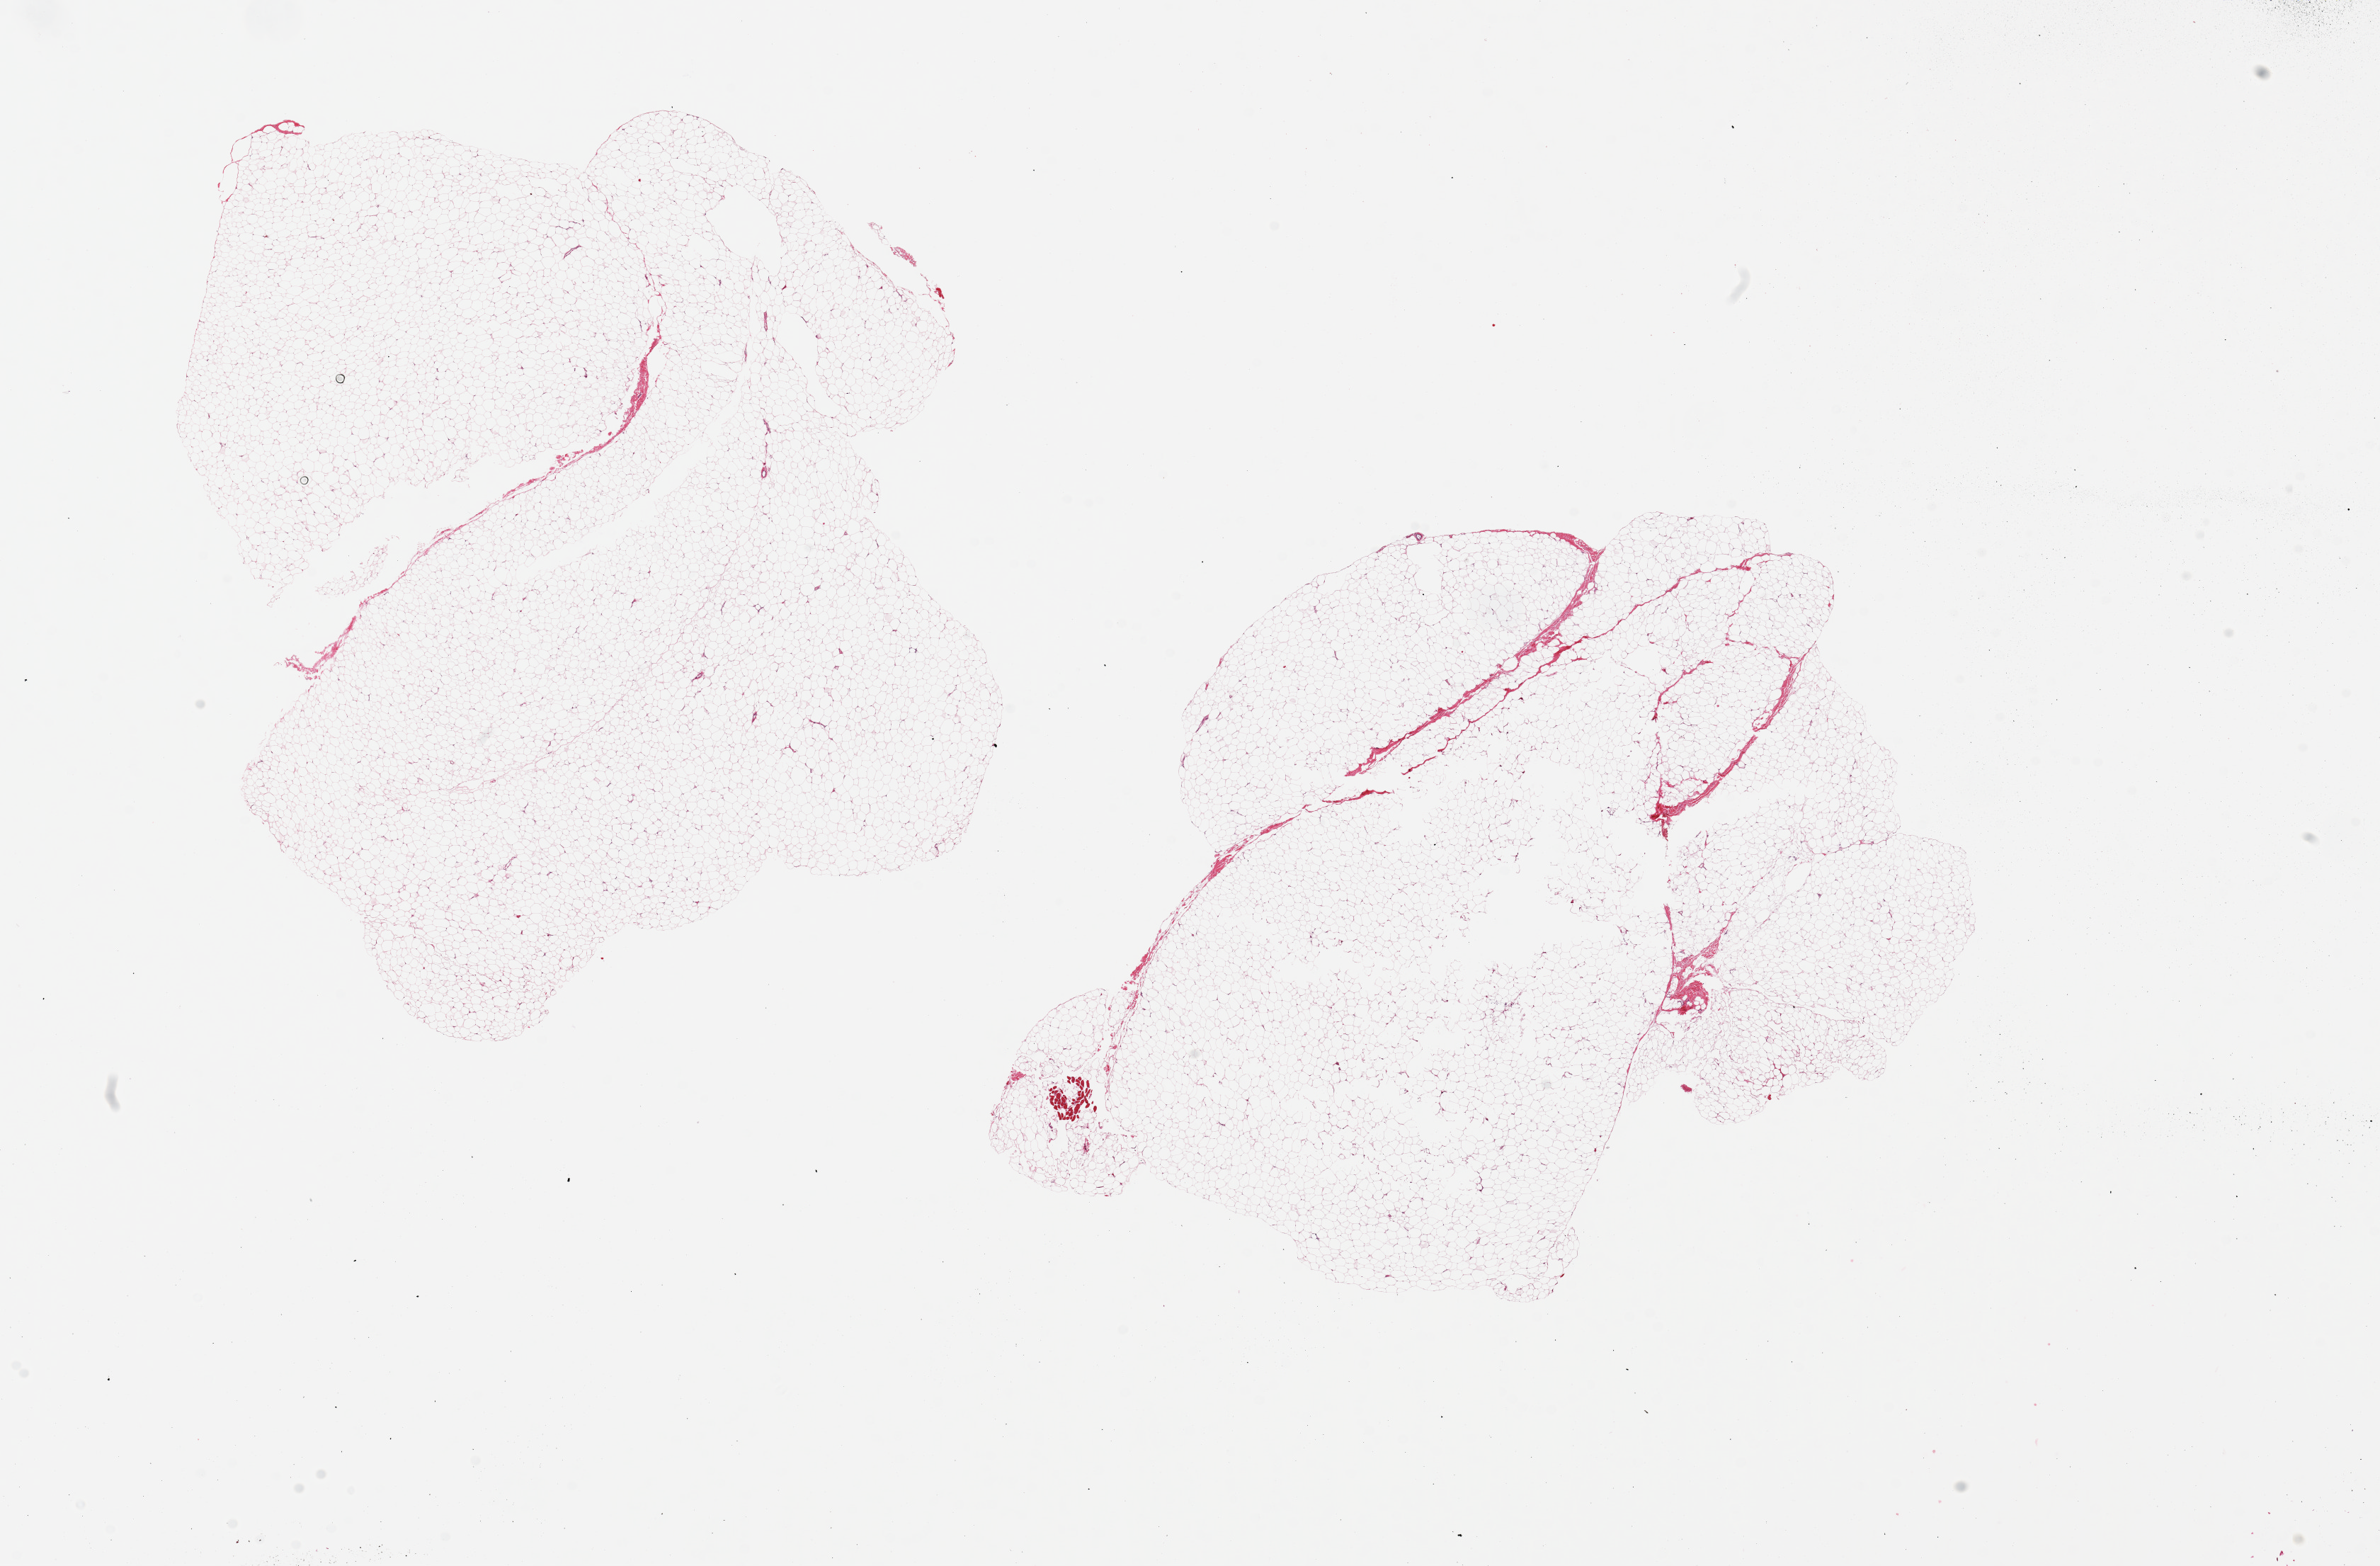
Digitized hematoxylin and eosin (H&E)-stained section — whole scanned area (about 26.6 x 17.5 mm, from a 20x scan) shown as a low-resolution overview; PAXgene-fixed paraffin-embedded (PFPE) section; section of breast (target tissue); donor tissue sample. Donor: male.
• reviewer comment on this tissue sample: 2 pieces, 11x10 & 11x8.5mm; all adipose tissue